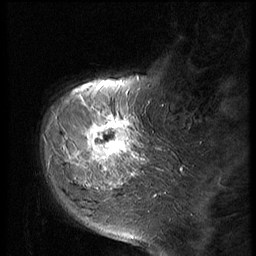
Breast MRI (dynamic contrast-enhanced), one sagittal slice; slice 14 of 56 in the series (ordered by position); dynamic contrast-enhanced series, image 2 of 2 at this slice position (ordered by acquisition); 1.5 T; TE 4.2 ms, TR 9 ms; 2.5 mm slice thickness; 256 × 256 image matrix, field of view 180 × 180 mm. Female patient, age 51 years. Case-level facts recorded for this patient, not image findings: setting: breast cancer imaged before/during neoadjuvant chemotherapy; receptor status: triple-negative.
Outlined on this slice (semi-automatic segmentation, software-assisted and operator-edited):
- analysis volume of interest (the breast-tissue region the enhancement analysis was run in; not a lesion): bounding box [x1, y1, x2, y2] px = [60, 98, 147, 197]
- tumour enhancement mask (voxels above the 140 % enhancement threshold inside the analysis volume of interest): [74, 102, 135, 175]